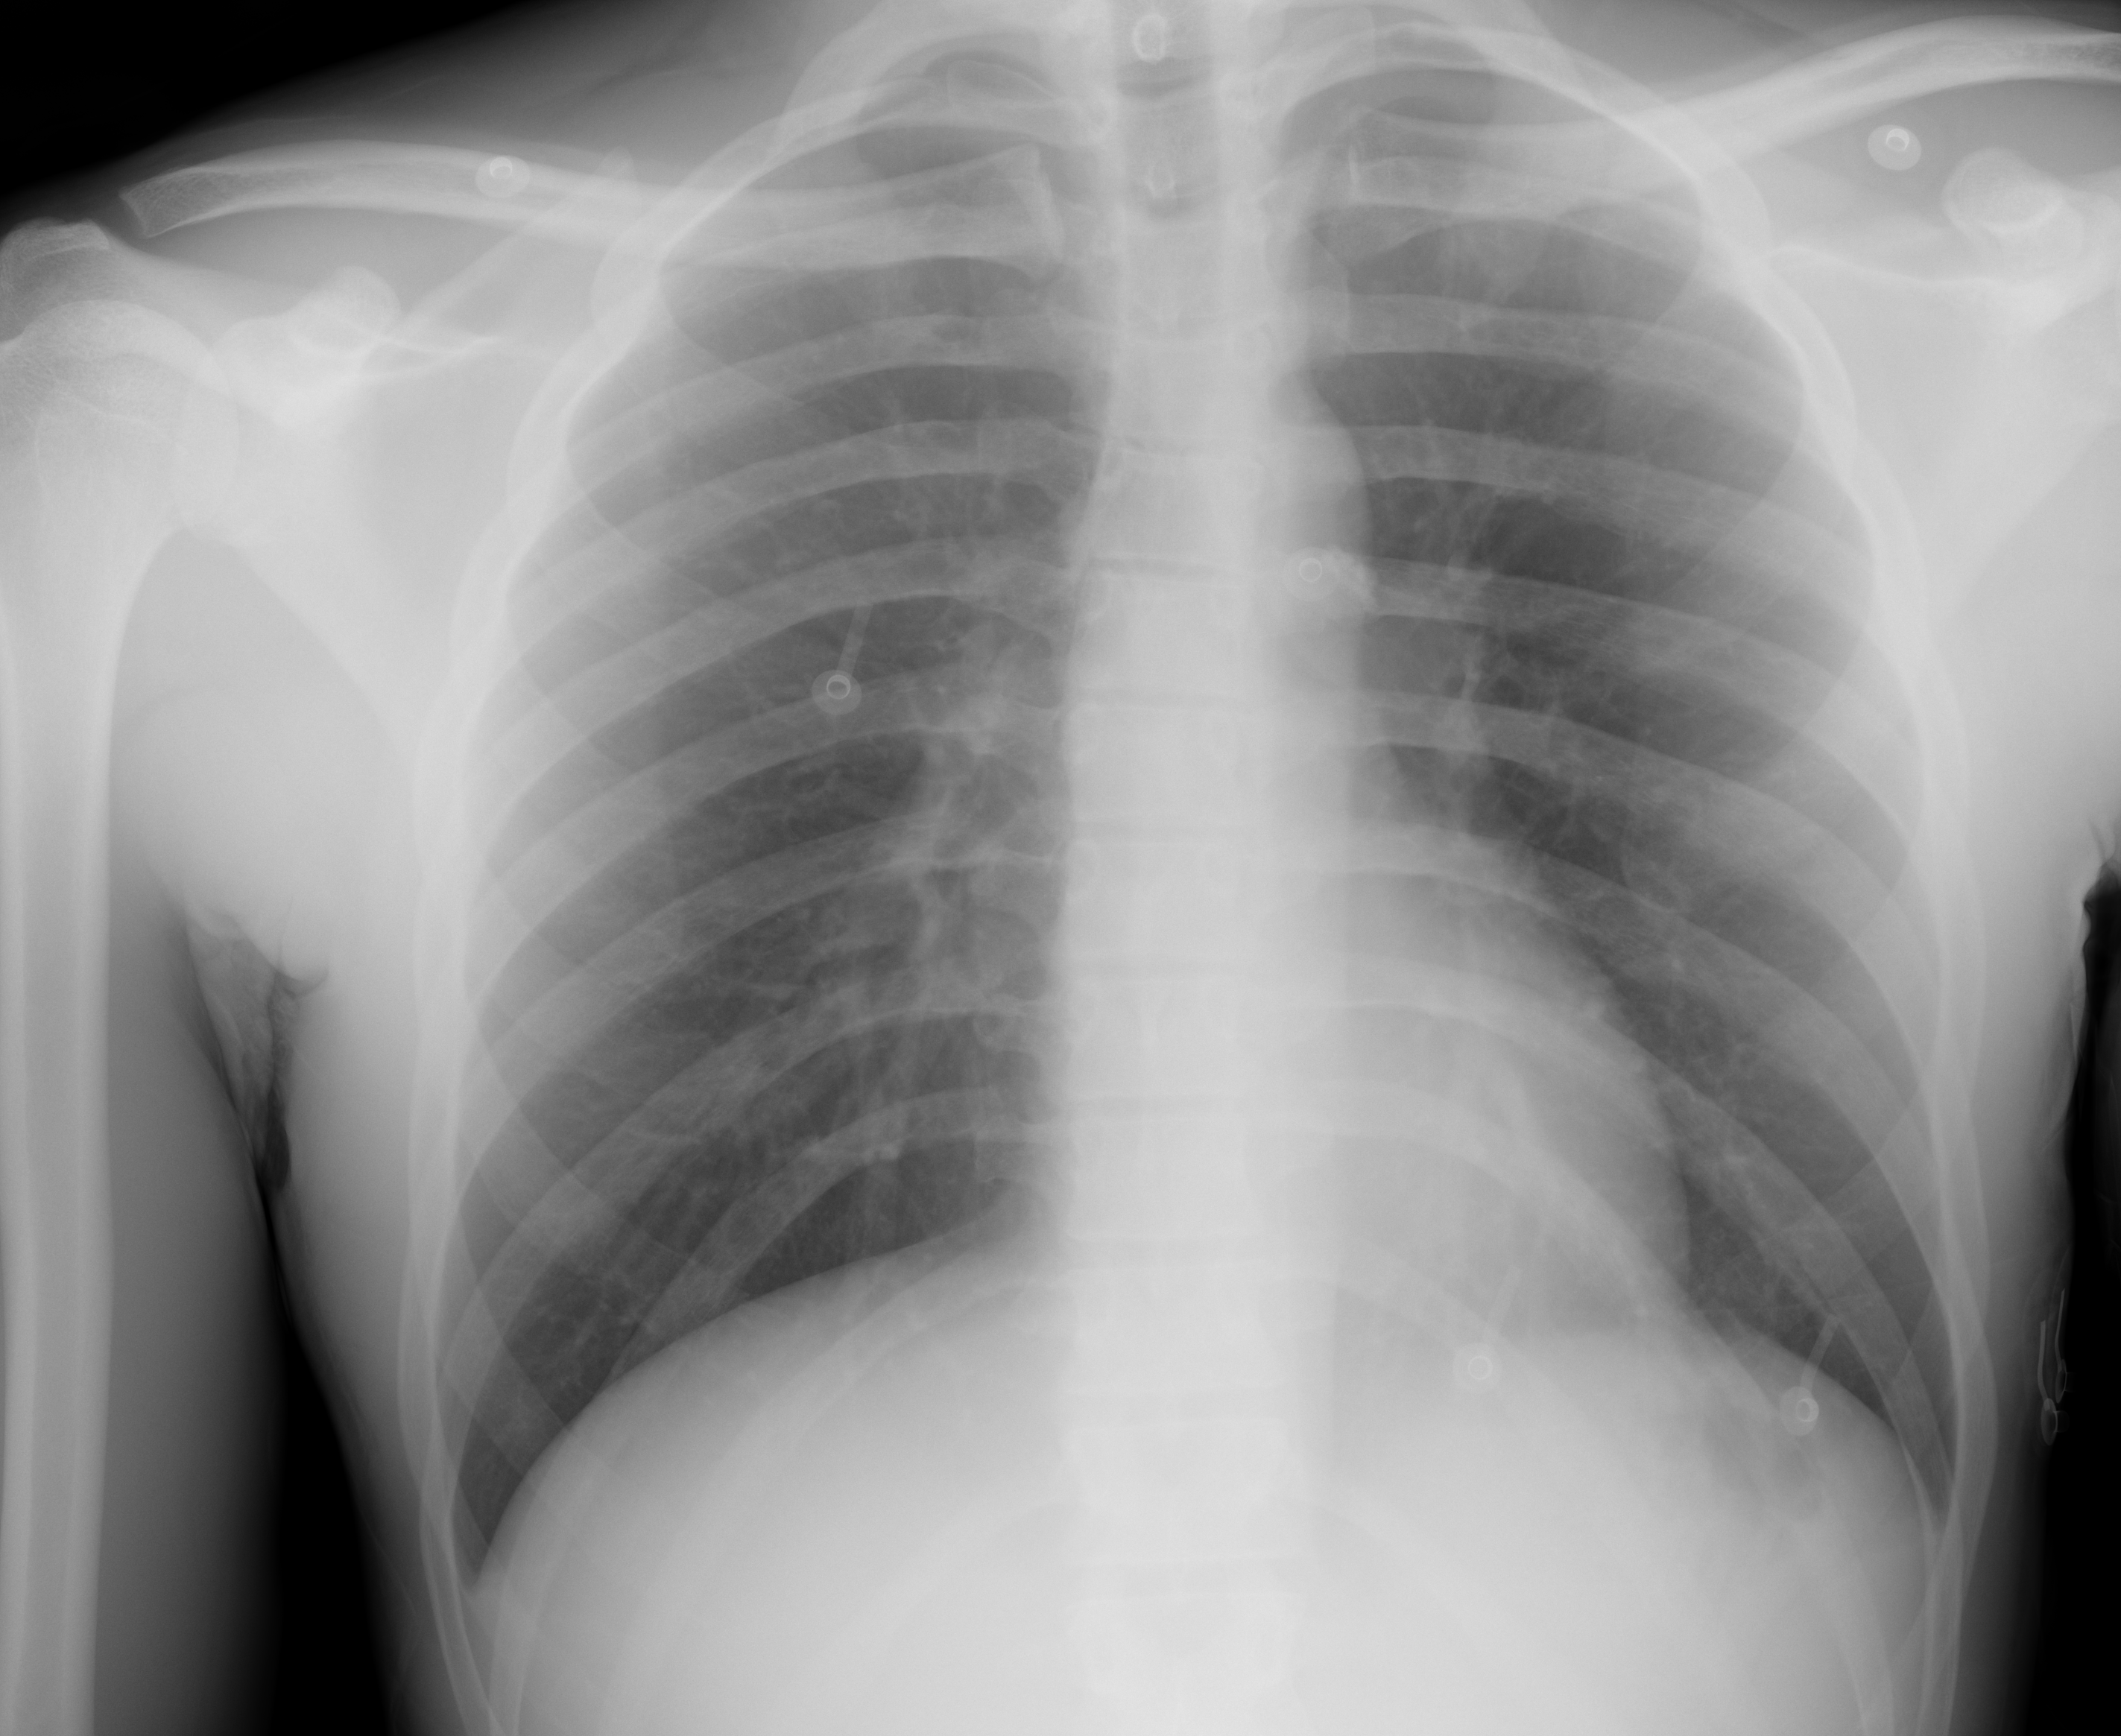
Chest X-ray (portable), AP projection. Male patient, age 19 years; imaged 1 day after the COVID-19 diagnosis.
Radiologist key findings (as recorded): The lungs are clear.